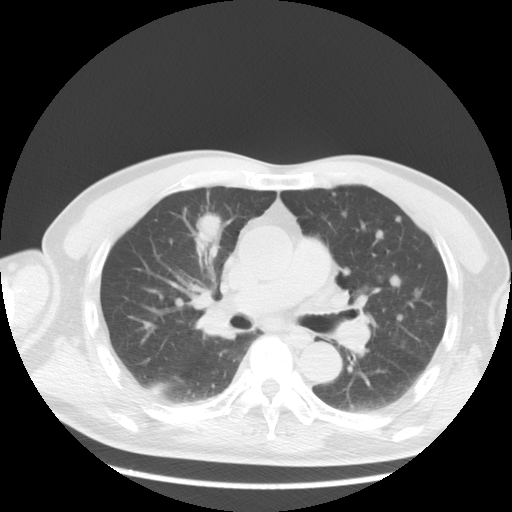
Chest CT, one axial slice; slice 12 of 36 in the series (ordered by position); reconstruction kernel STANDARD; 120 kVp; lung window (W 1500 / L -600 HU); 512 × 512 image matrix. Patient: male, 57 years. From the clinical record (not read from this slice): clinical TNM (as recorded): T2 N3 M1a.
Annotated regions visible in this slice (bounding box drawn by a radiologist):
- lung tumour (recorded histology: adenocarcinoma): bounding box [x1, y1, x2, y2] px = [194, 212, 218, 243]